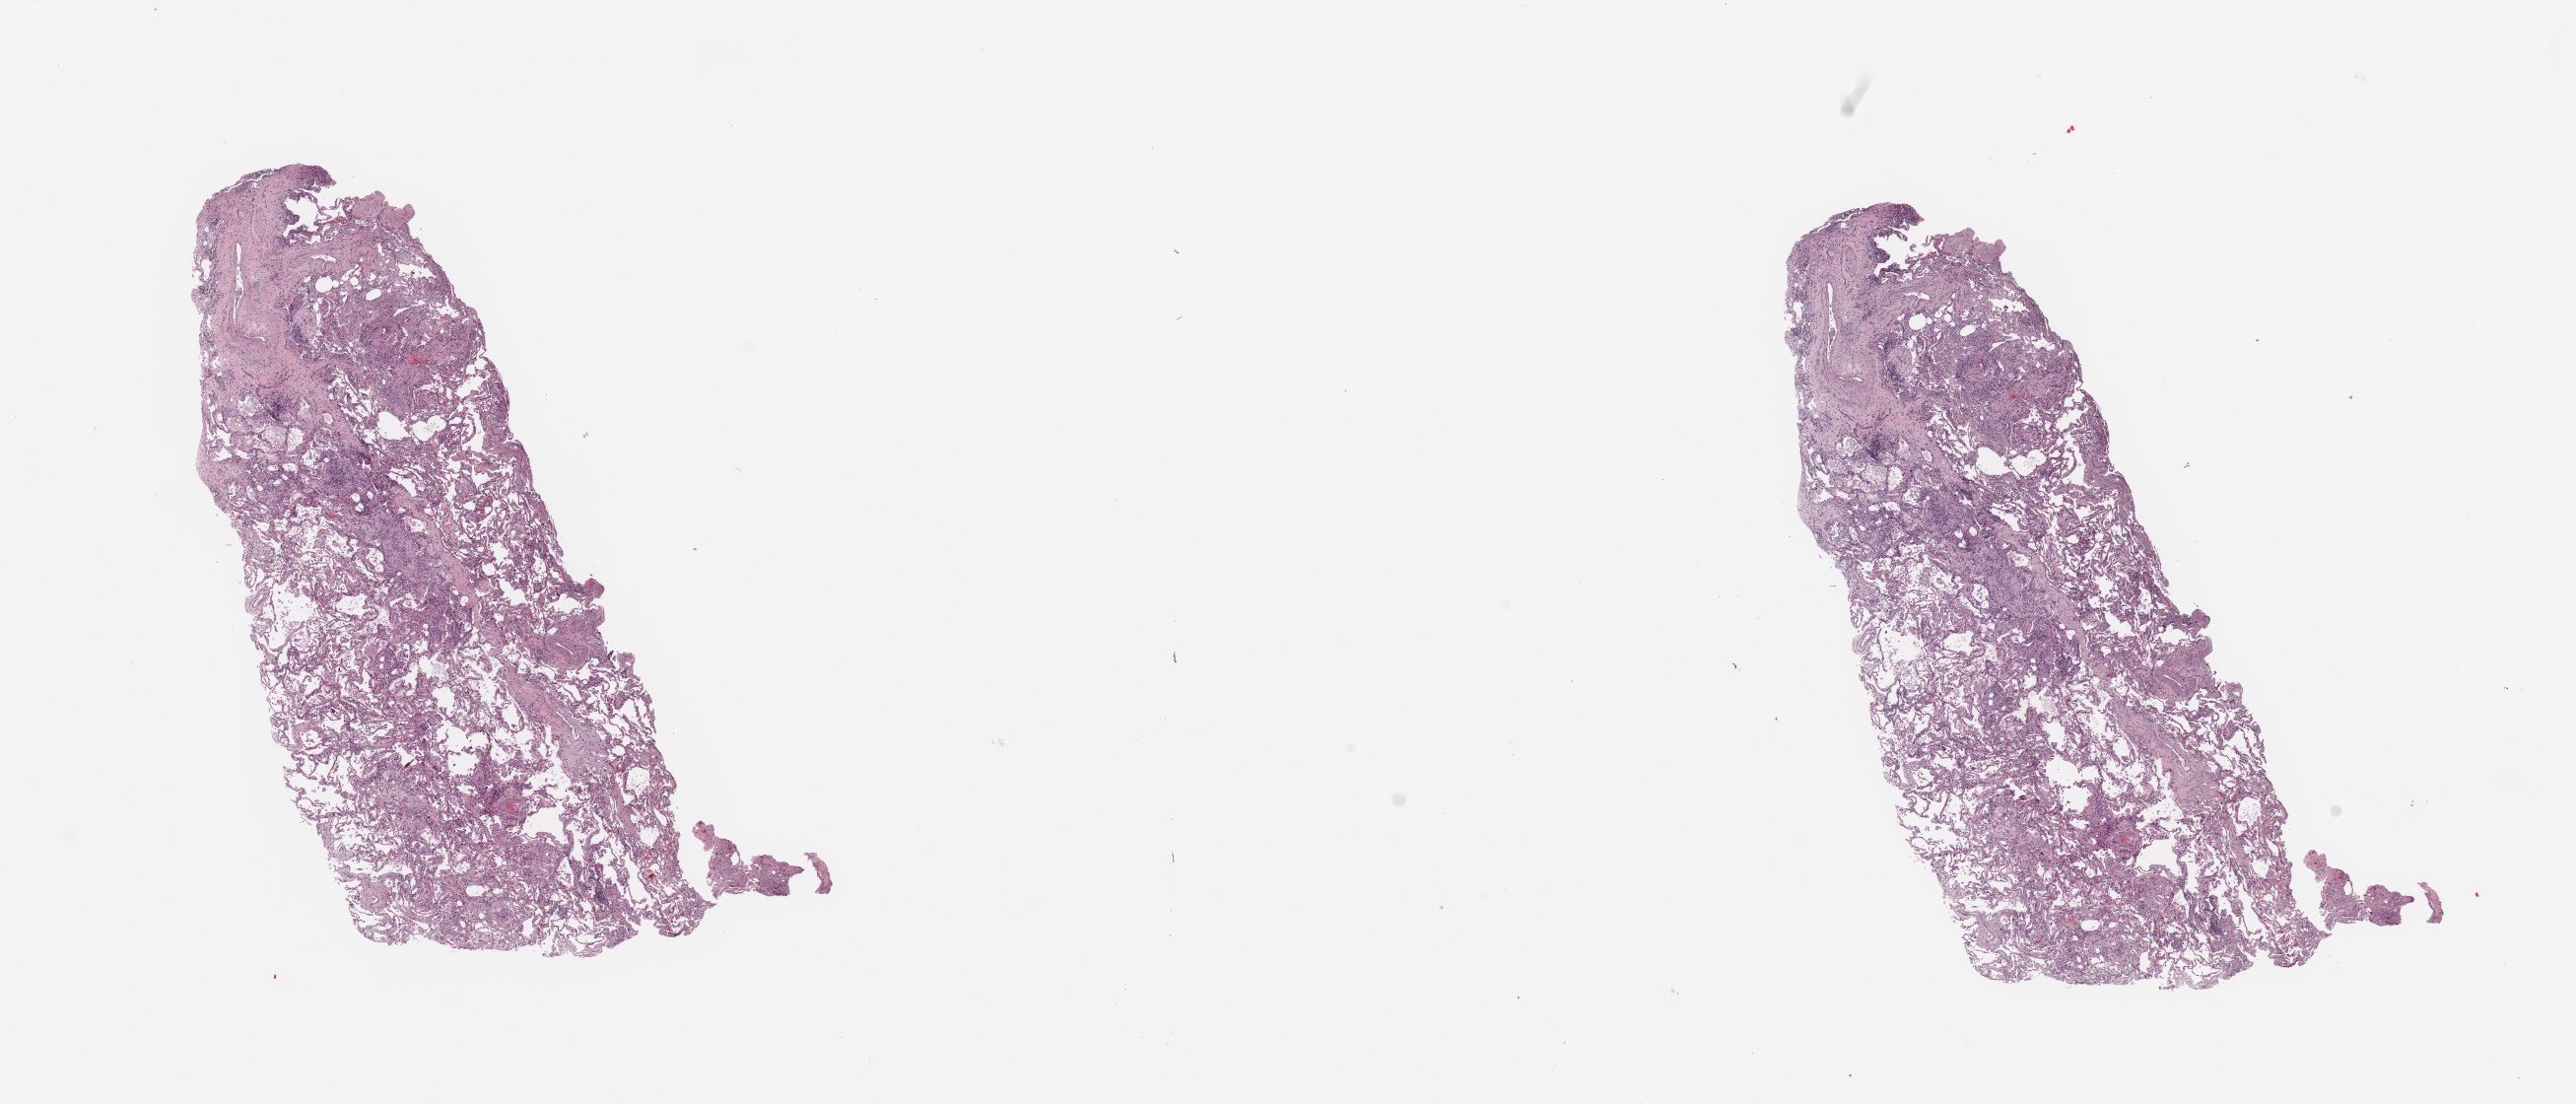
Digitized H&E tissue section (whole slide) — a low-resolution overview of the entire scanned area, about 20.7 x 8.9 mm, normal (non-tumour) tissue sample, sampled site: lung. Patient: female, age 79 years.
This section: normal (non-tumour) tissue from the same patient. Patient diagnosis: Adenocarcinoma, NOS.